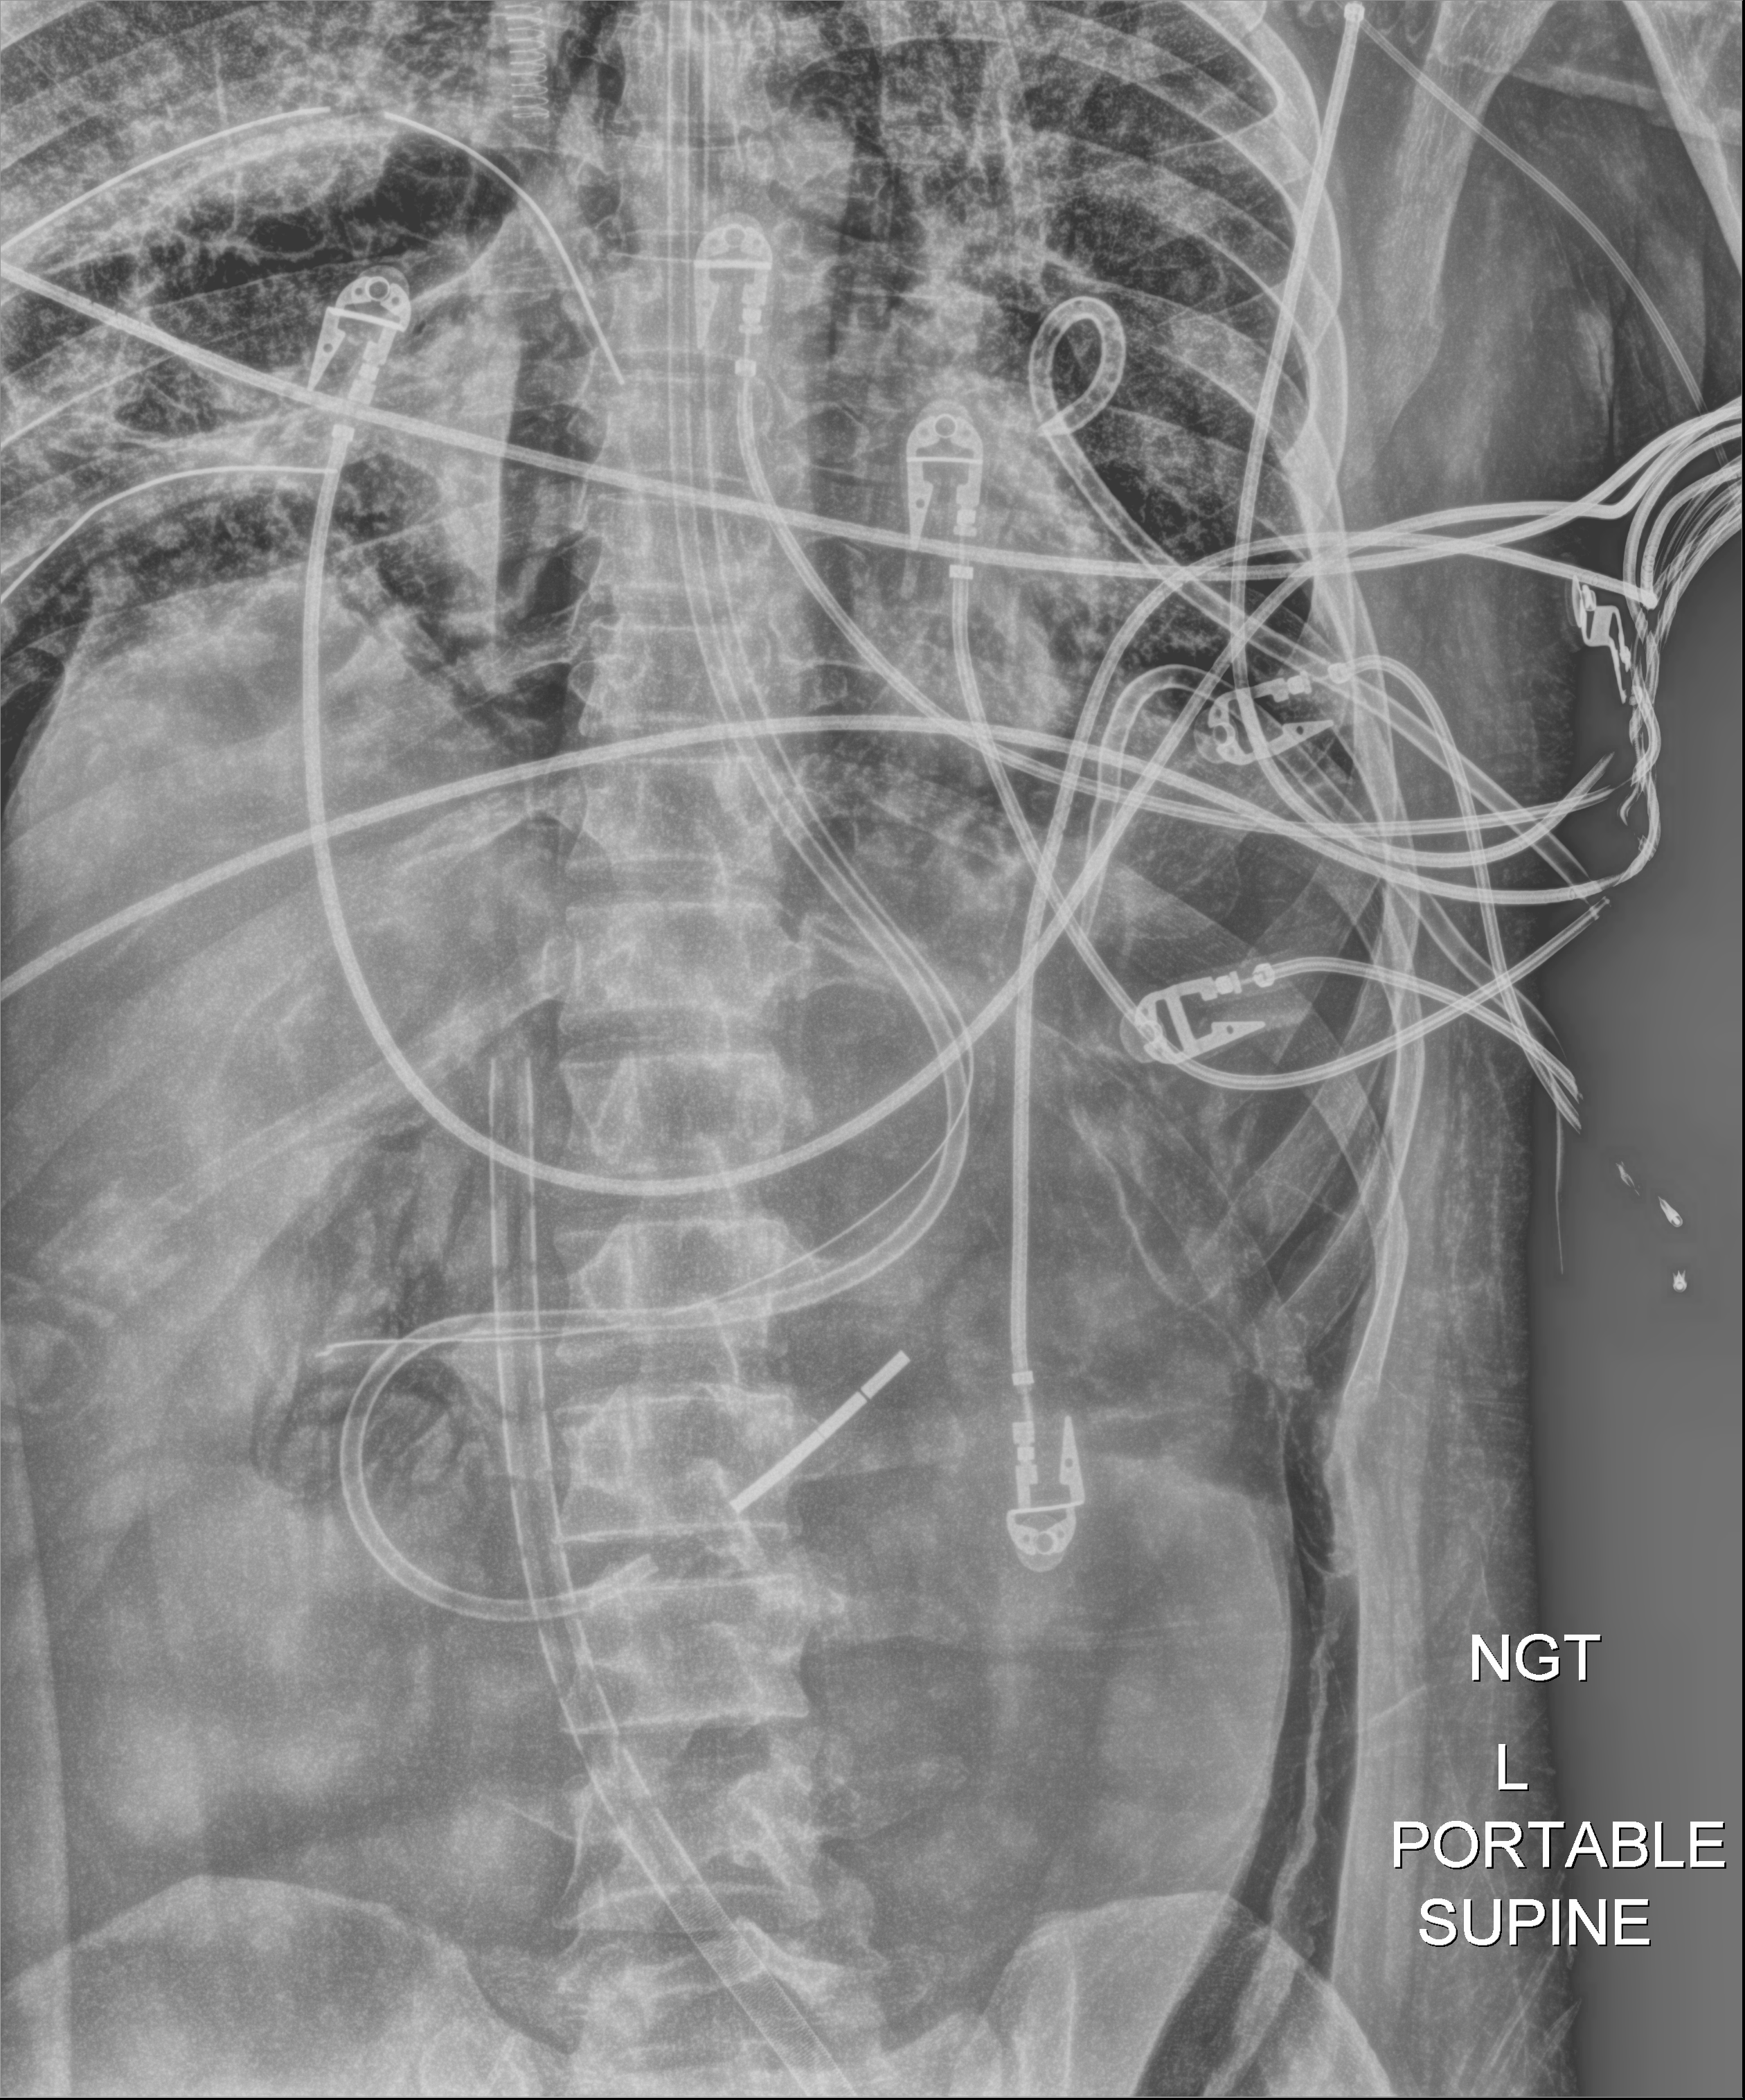
Abdomen X-ray (portable), anteroposterior (AP) projection. Adult patient hospitalised with COVID-19, age 18–59 years.
From the hospital-stay record, not from the radiograph (when in the stay this image was taken is not recorded): length of hospital stay: 60 days; admitted to intensive care during this hospital stay: yes; mechanically ventilated during this hospital stay: yes.